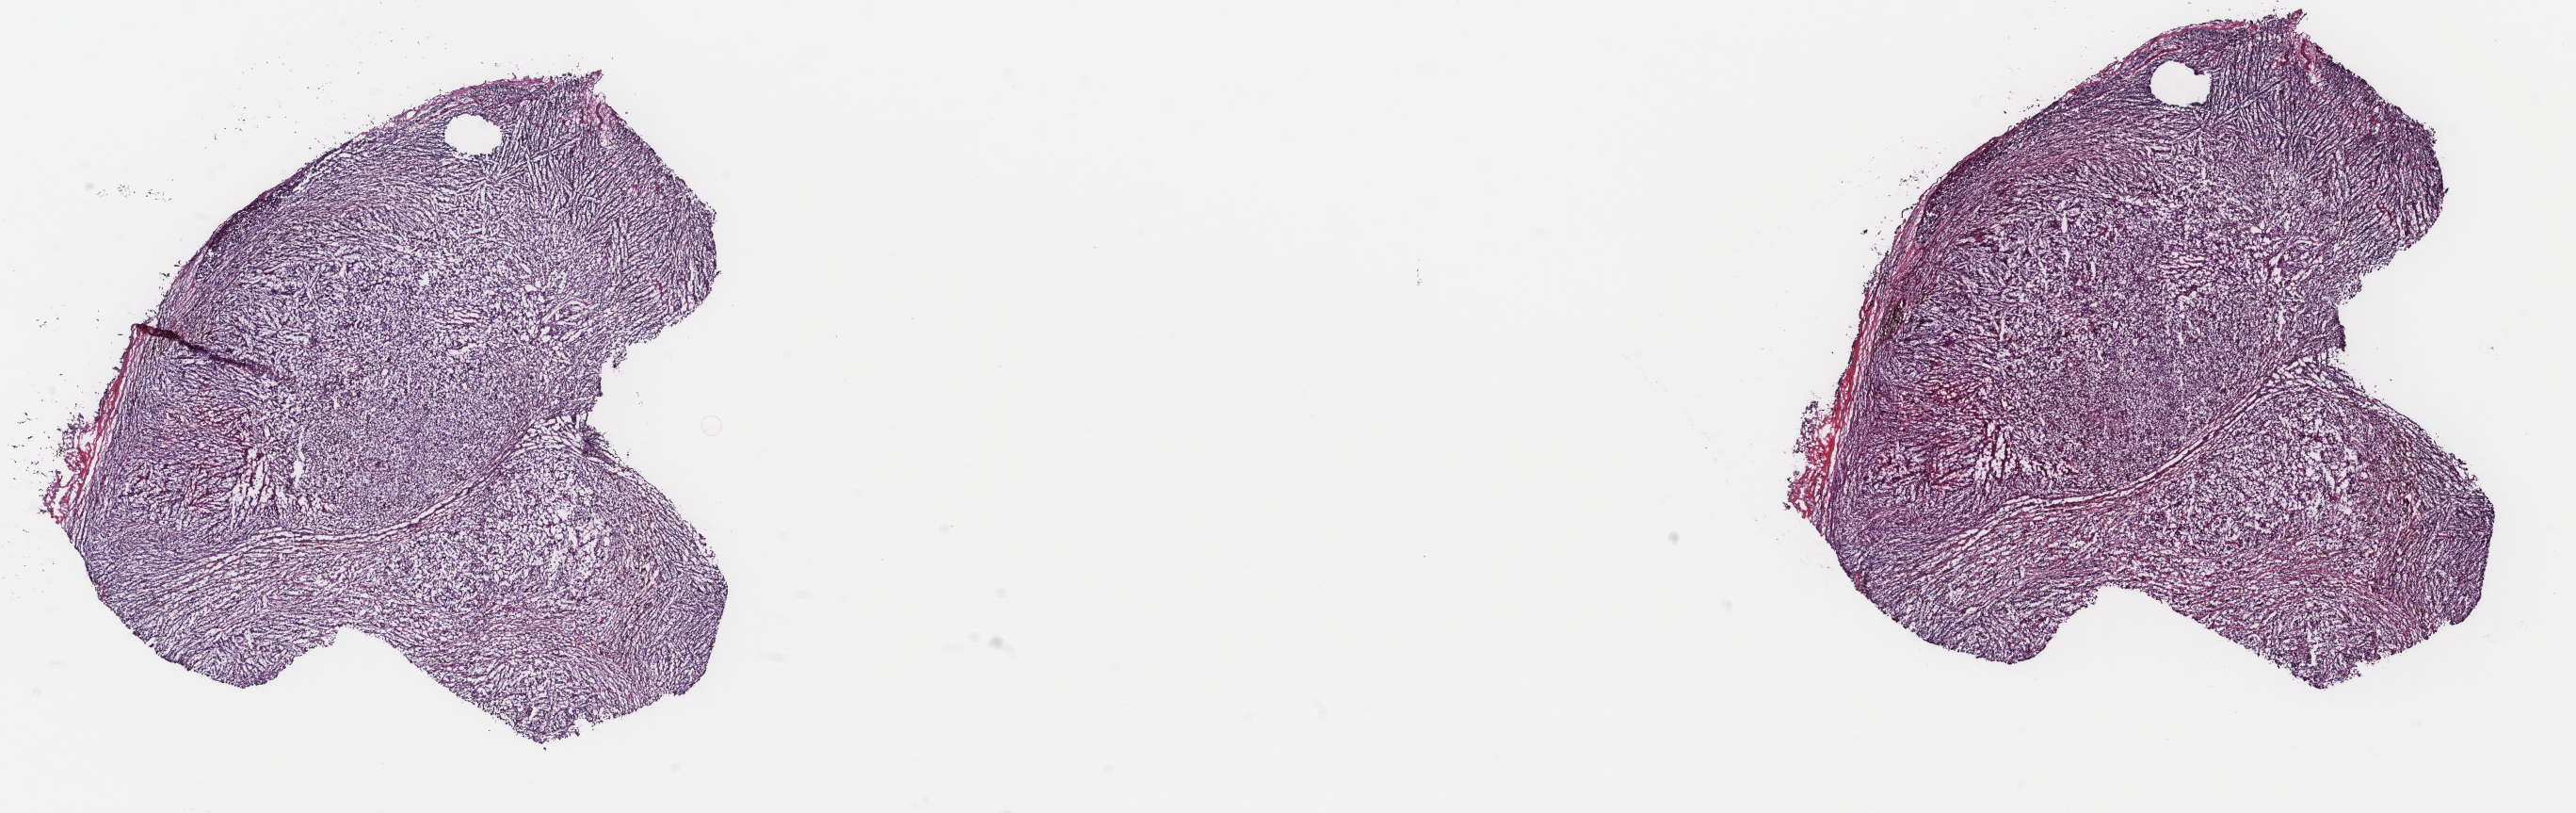
H&E whole-slide image, whole scanned area (about 21.7 x 6.9 mm, from a 40x scan) shown as a low-resolution overview. Frozen section. Metastatic tumour sample. Patient: female, age at initial diagnosis 58 years. Slide review estimates, as recorded: tumour cells 100%, tumour nuclei 95%, normal cells 0%, stromal cells 0%, necrosis 0%. Inflammatory infiltration, as recorded: lymphocyte infiltration 0%, monocyte infiltration 0%, neutrophil infiltration 0%.
This section: metastatic tumour tissue. Patient diagnosis: Malignant melanoma, NOS.